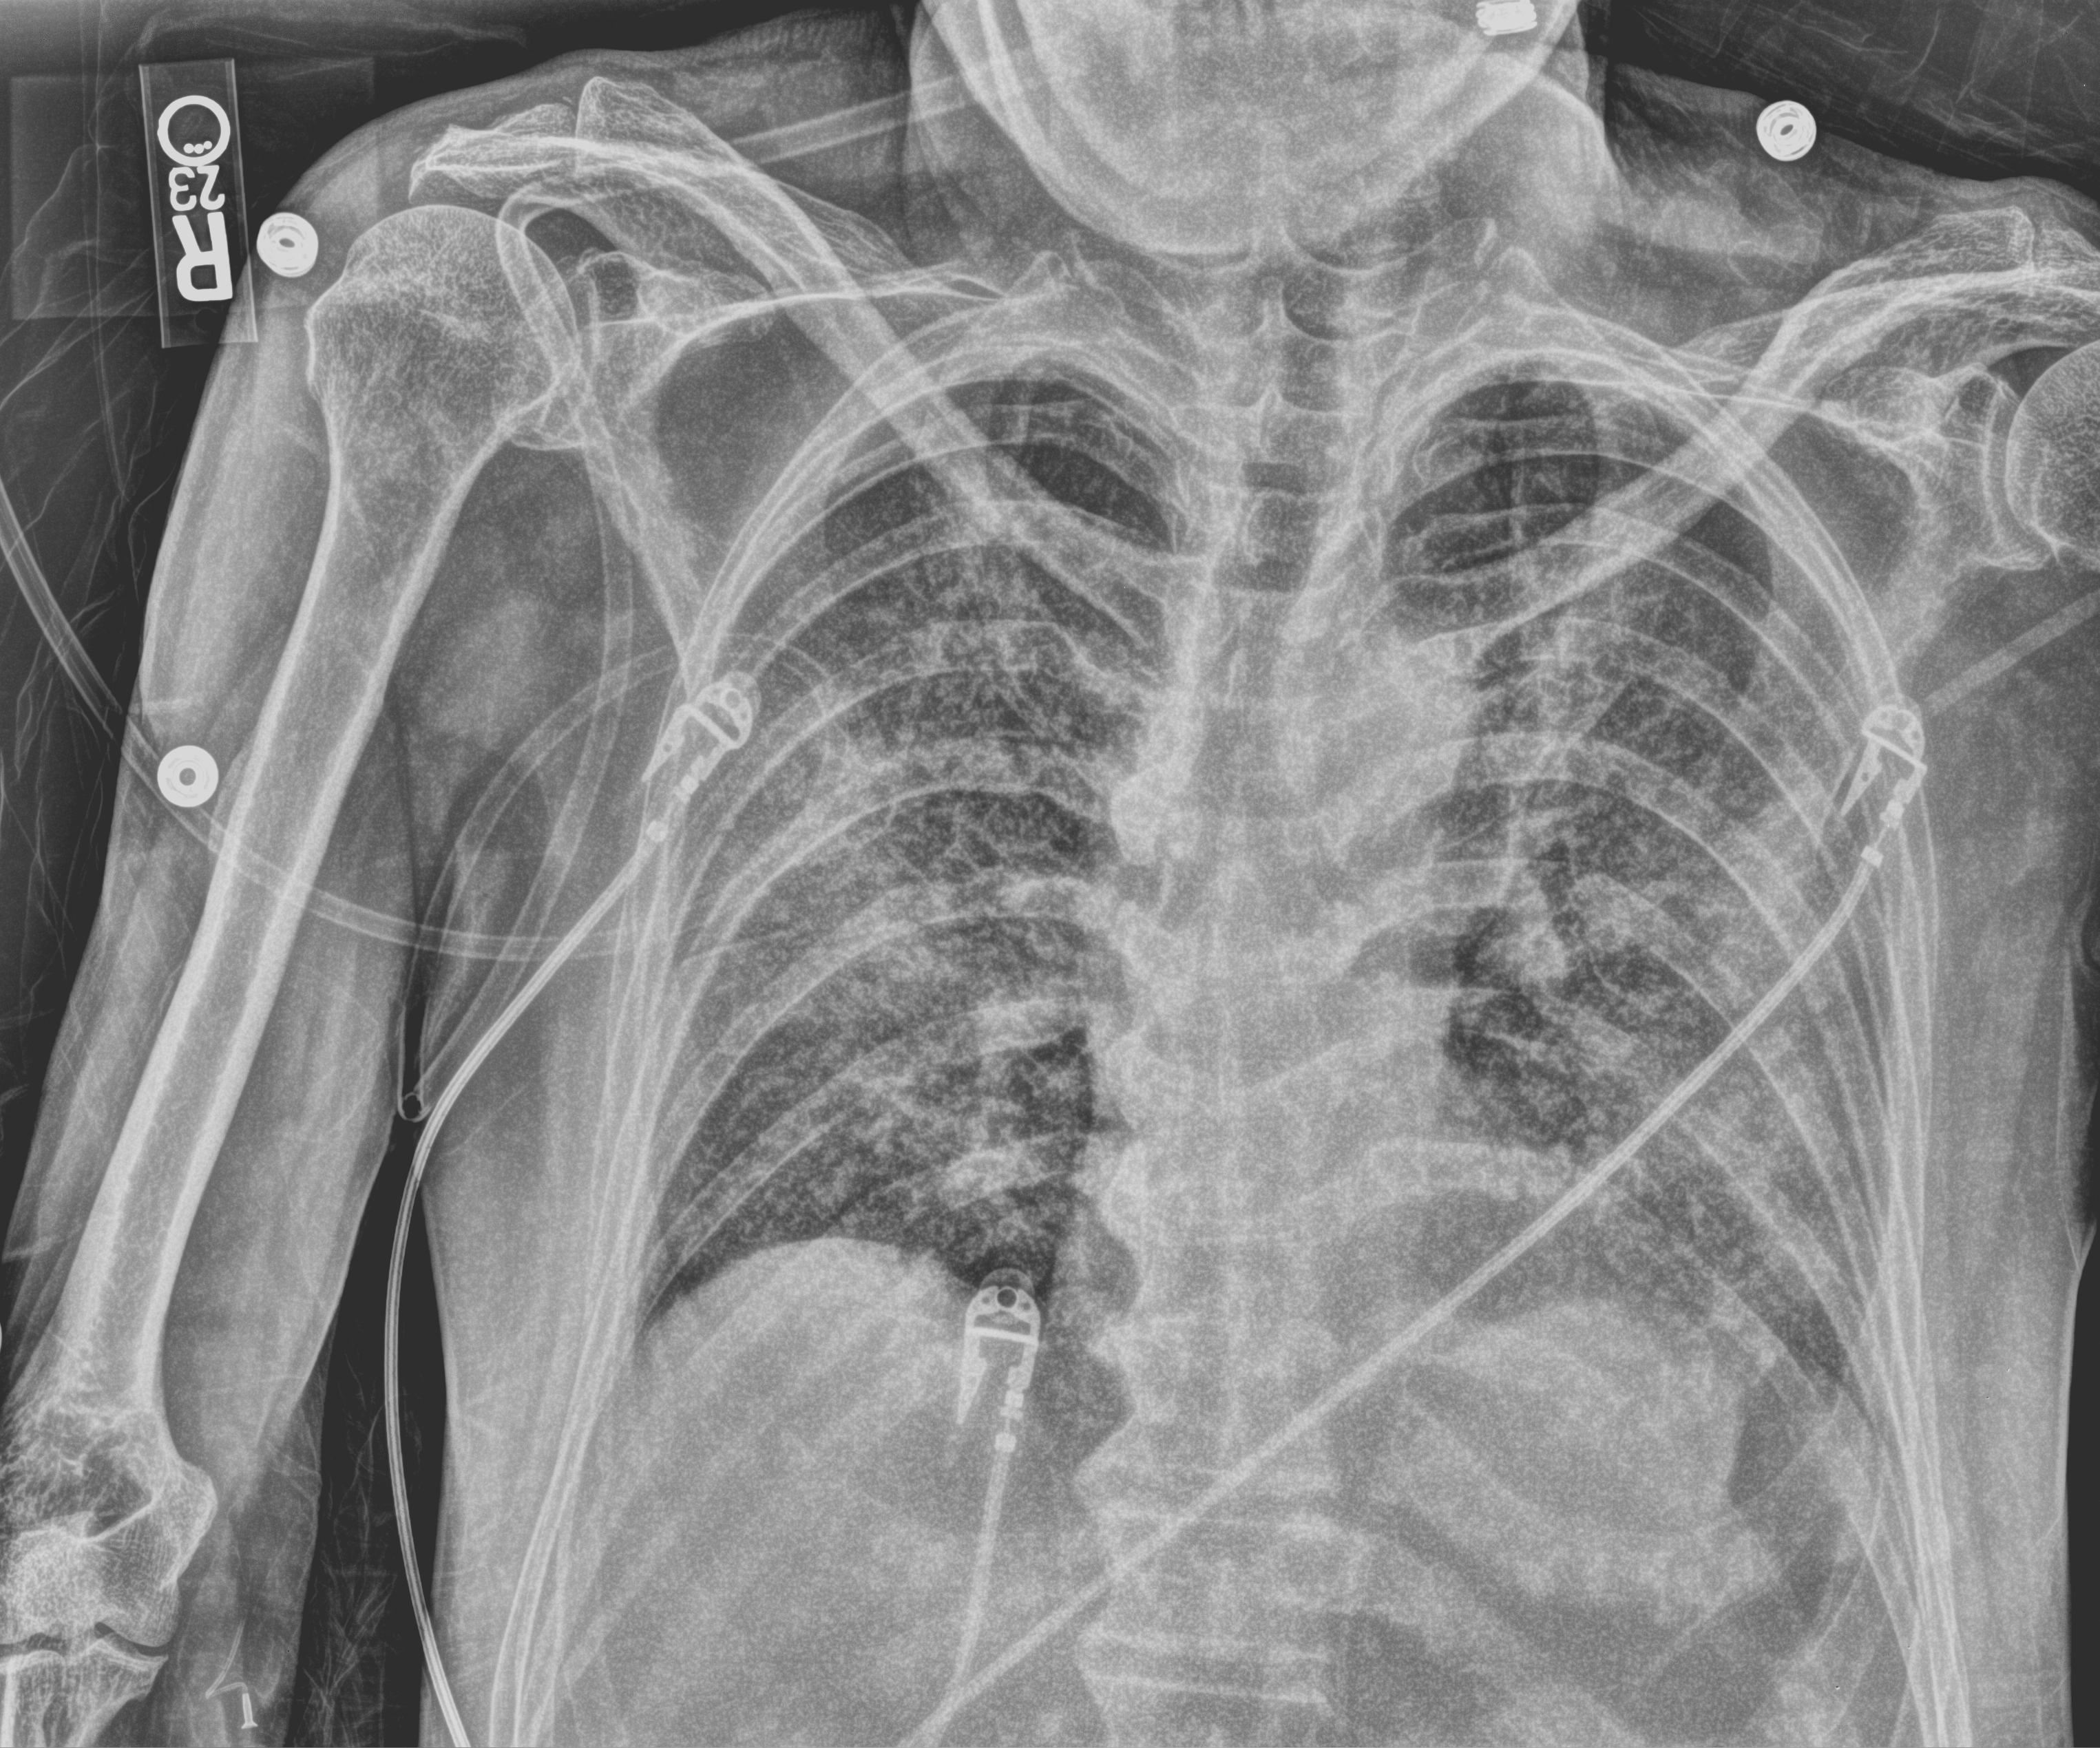
Portable chest radiograph, anteroposterior (AP) projection. Patient hospitalised with COVID-19; male, aged 60–74 years.
Admission-level facts for this patient (not findings on this image; timing relative to this image not recorded): admitted to intensive care during this hospital stay: yes; diabetes (admission record): yes.